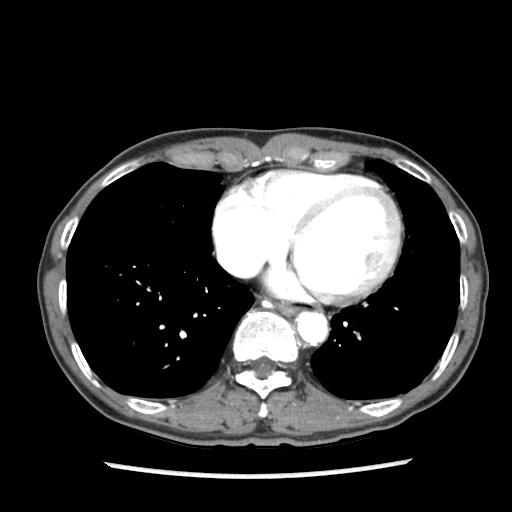
Contrast-enhanced abdominal CT (liver protocol), one axial slice; slice 84 of 87 in the series (ordered by position); reconstruction kernel STANDARD; 140 kVp; soft-tissue window (W 400 / L 40 HU); 2.5 mm slice thickness; 512 × 512 image matrix. From the clinical record (not read from this slice): diagnosis: hepatocellular carcinoma (patient treated with transarterial chemoembolisation; whether this scan precedes or follows treatment is not stated here); TNM stage (as recorded): Stage-IIIB; Child-Pugh class: A; tumour differentiation: well differentiated; tumour nodularity: uninodular.
Structures marked on this image (semi-automatic segmentation, software-assisted and operator-edited):
- abdominal aorta: bounding box <298,312,326,343> (left, top, right, bottom; pixels)